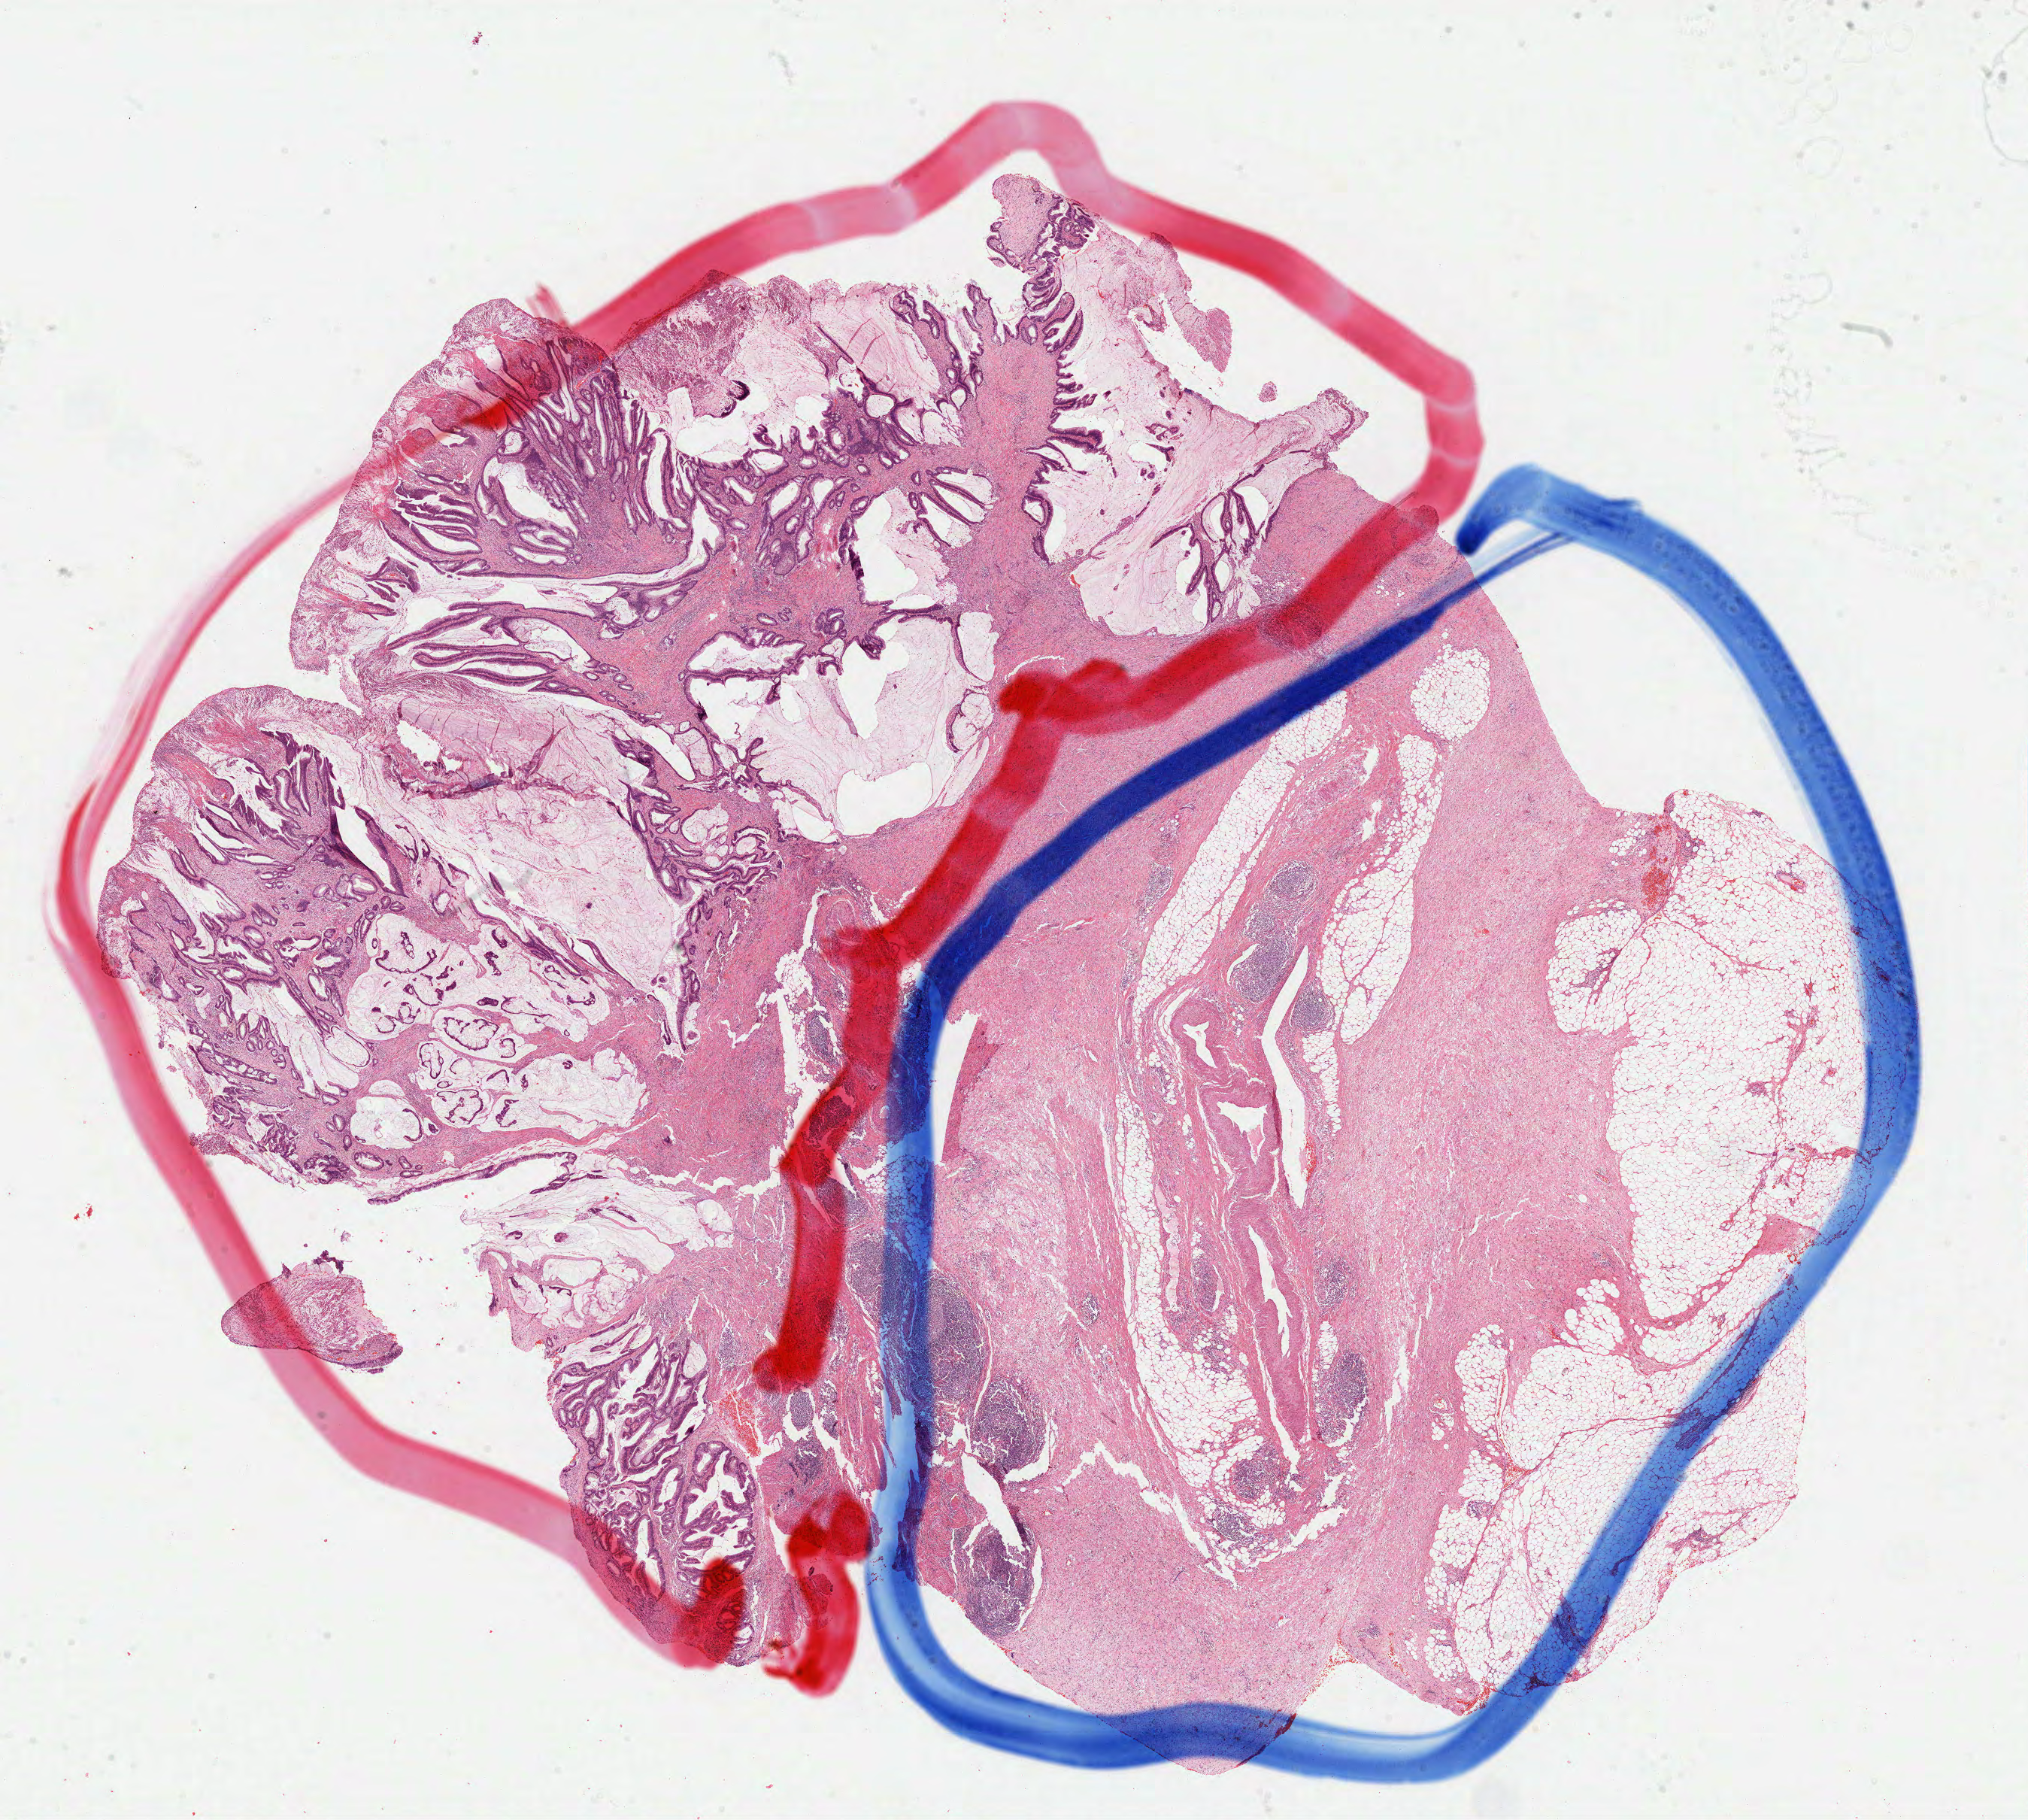
Digitized H&E-stained tissue section (whole slide) — a low-resolution overview of the entire scanned area, about 21.8 x 19.5 mm (slide scanned at 40x). FFPE section. Colon, primary tumour sample. Patient: male, age at initial diagnosis 45 years.
AJCC pathologic stage: I (7th edition). Lymph nodes positive (case pathology): 0 of 21 examined. Diagnosis: Mucinous adenocarcinoma (cecum).